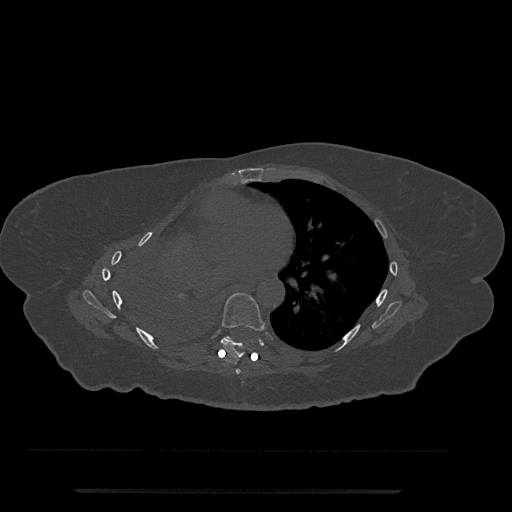
CT including the spine, one axial slice. Slice 435 of 797 in the series (ordered by position). Reconstruction kernel Br40s/3. 120 kVp. Bone window (W 1800 / L 400 HU). 0.5 mm slice thickness. 512 × 512 image matrix. Patient: female, 51 years. From the clinical record (not read from this slice): primary cancer: neuro; vertebrae with lytic lesions (as recorded): T8.
Annotated regions visible in this slice (semi-automatically segmented with operator editing):
- T6 vertebra: bounding box (x1, y1, x2, y2) in pixels: (235, 369, 241, 374)
- T7 vertebra: (221, 293, 265, 358)
- T8 vertebra: (224, 337, 230, 339)